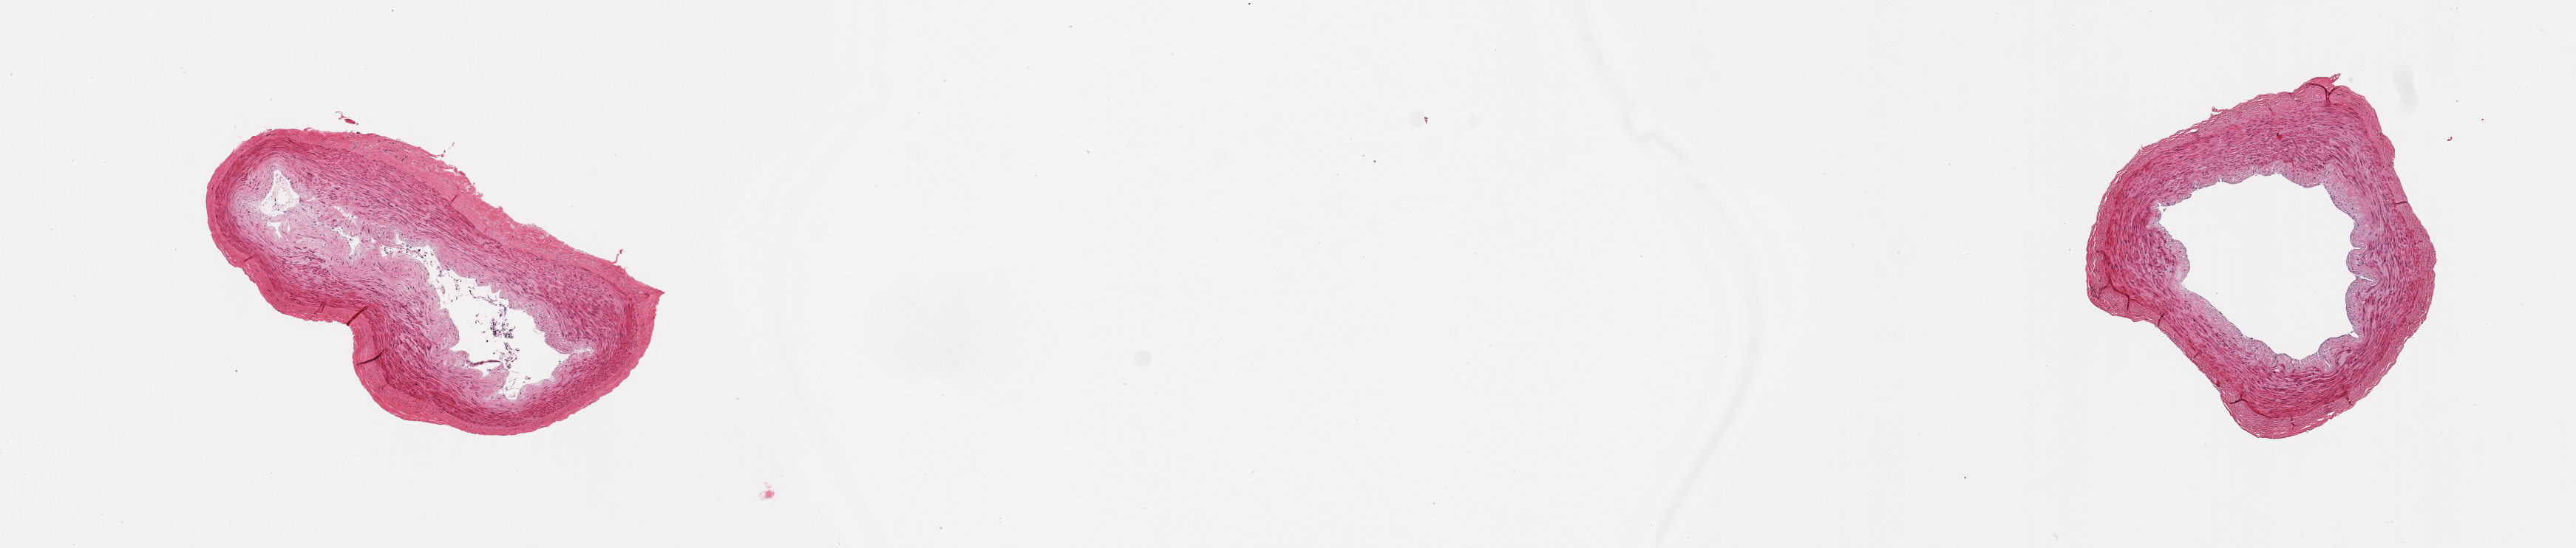
H&E whole-slide image, brightfield, whole scanned area (about 13.8 x 2.9 mm) shown as a low-resolution overview, PAXgene-fixed paraffin-embedded (PFPE) section, section of tibial artery (target tissue), donor tissue sample. Male donor.
Review note (as recorded): 2 pieces; well trimmed; eccentric plaque.